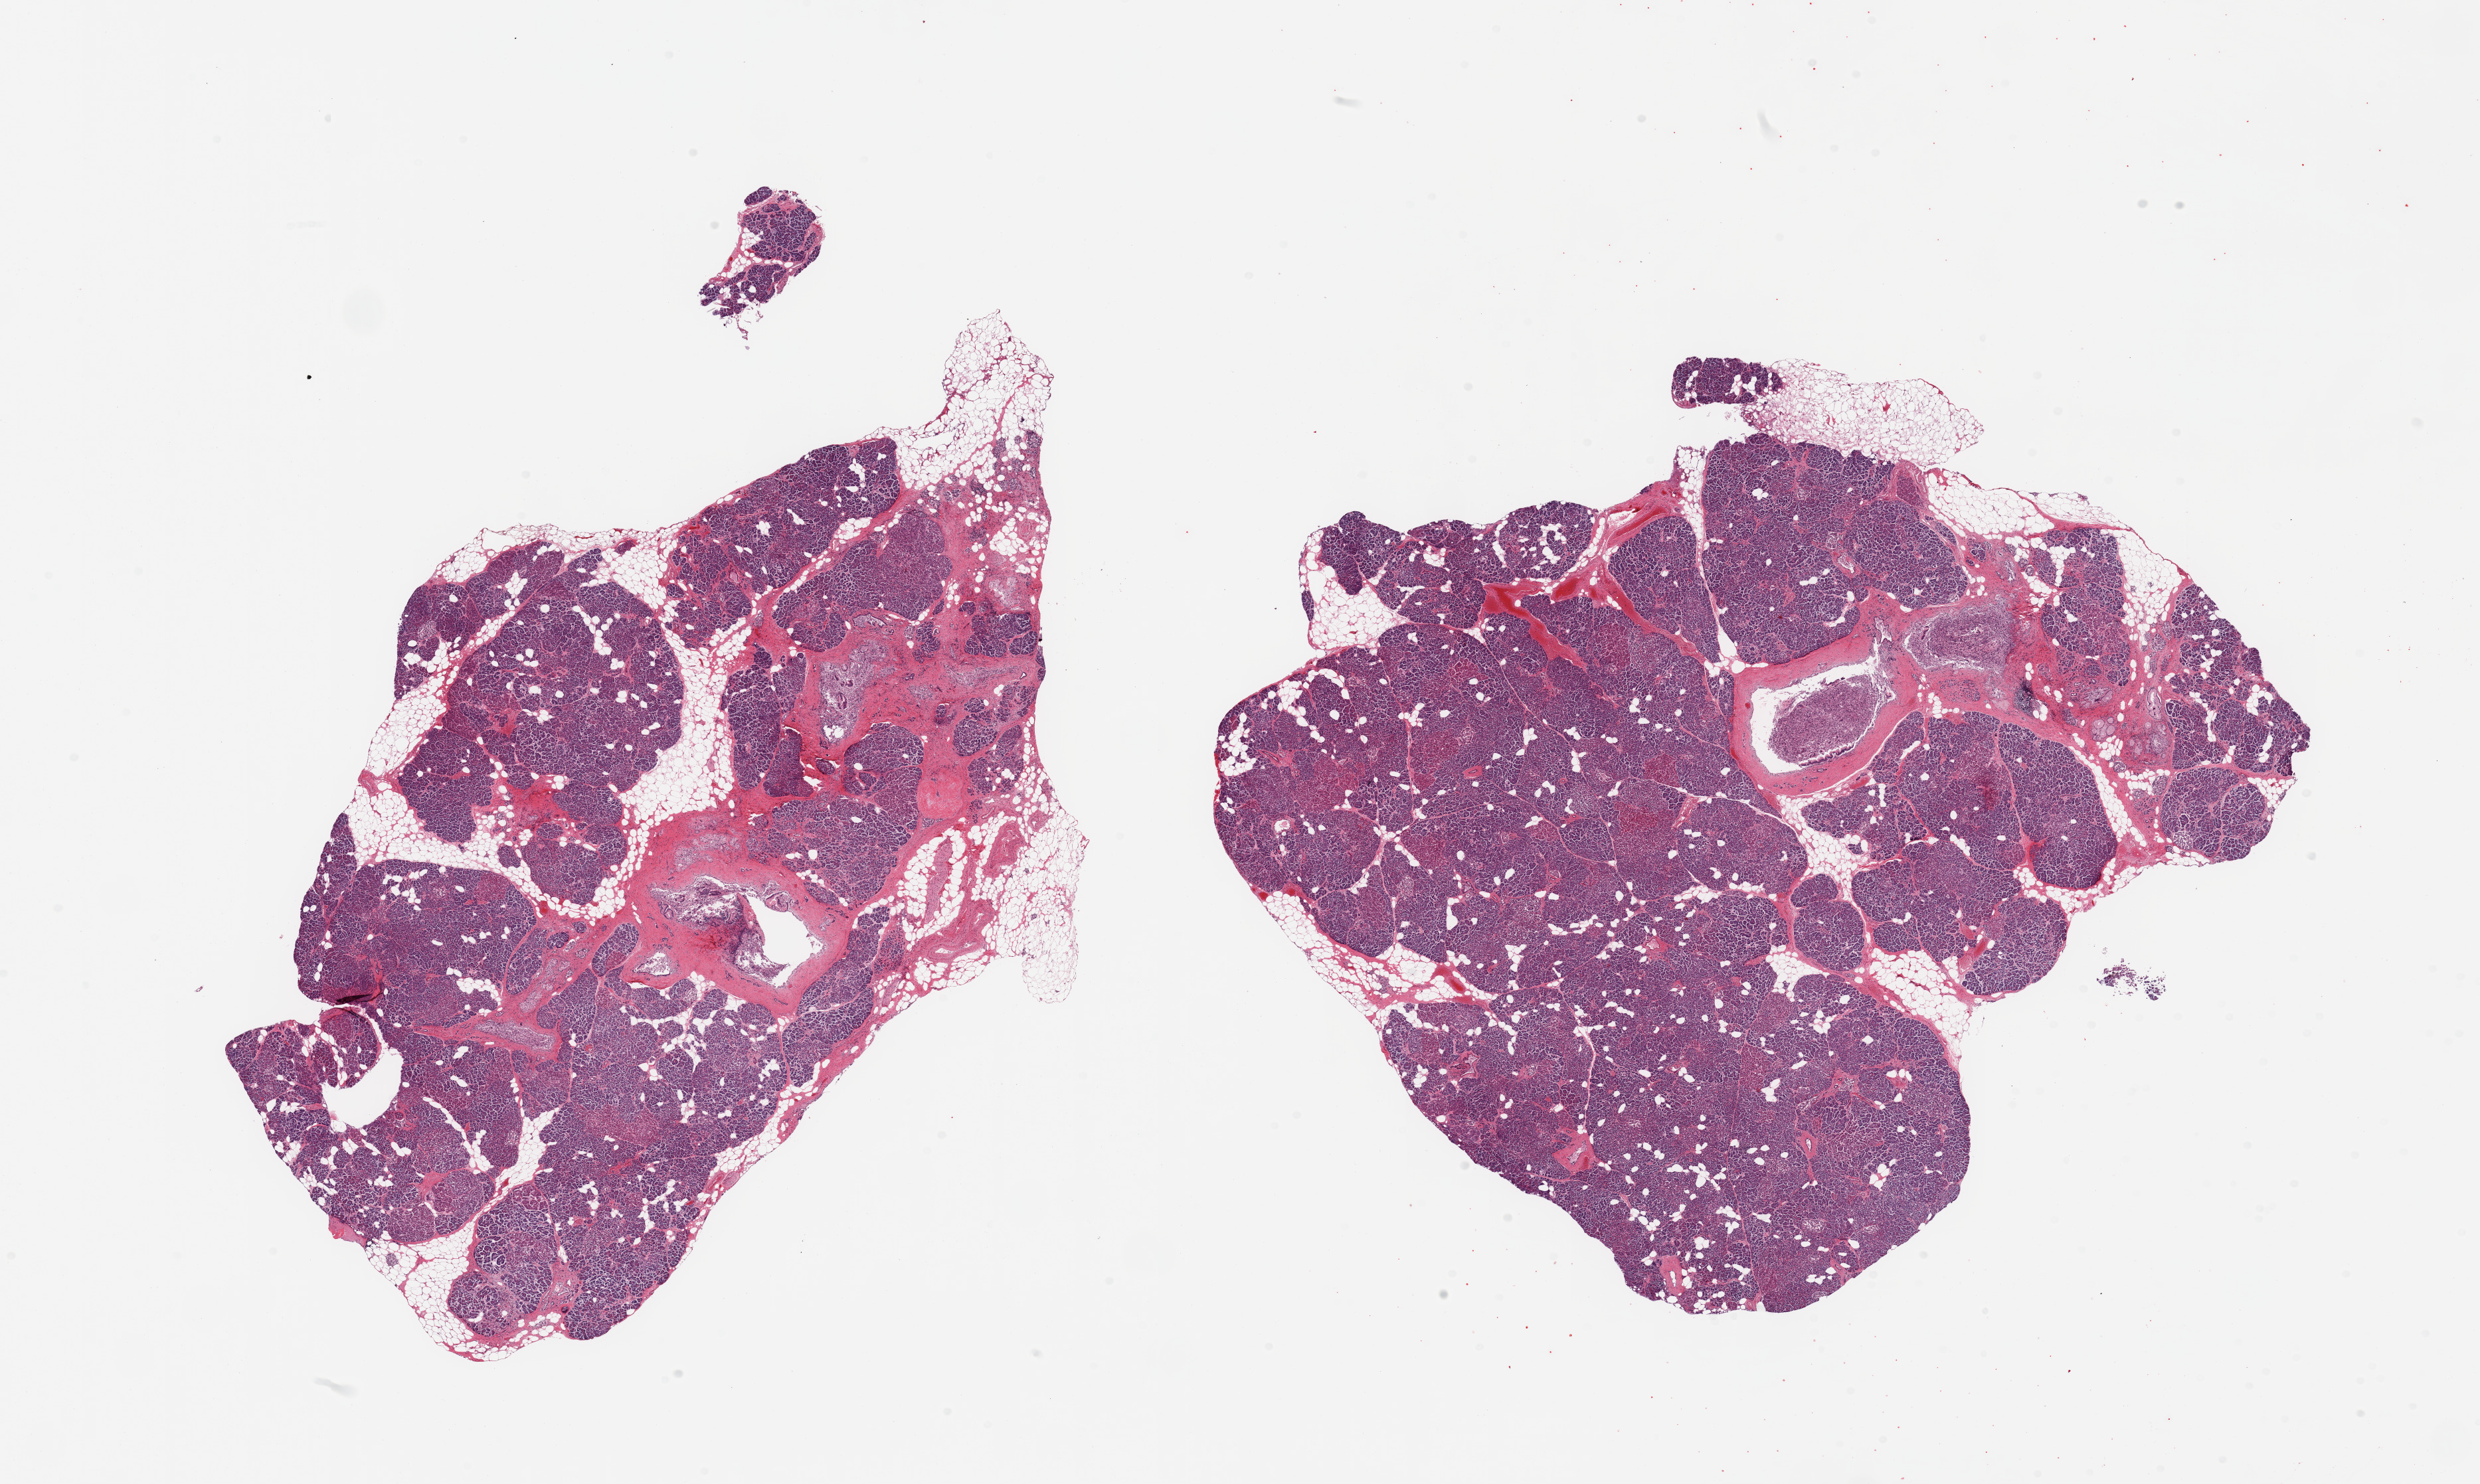
H&E whole-slide image, shown as a low-resolution overview of the whole scanned area (about 29.5 x 17.7 mm). PAXgene-fixed, paraffin-embedded tissue. Target tissue: pancreas. Tissue donor sample. Male donor.
Reviewer comment on this tissue sample: 2 pieces, moderate, approaching marked saponification; Islets degenerated, barely discernable.